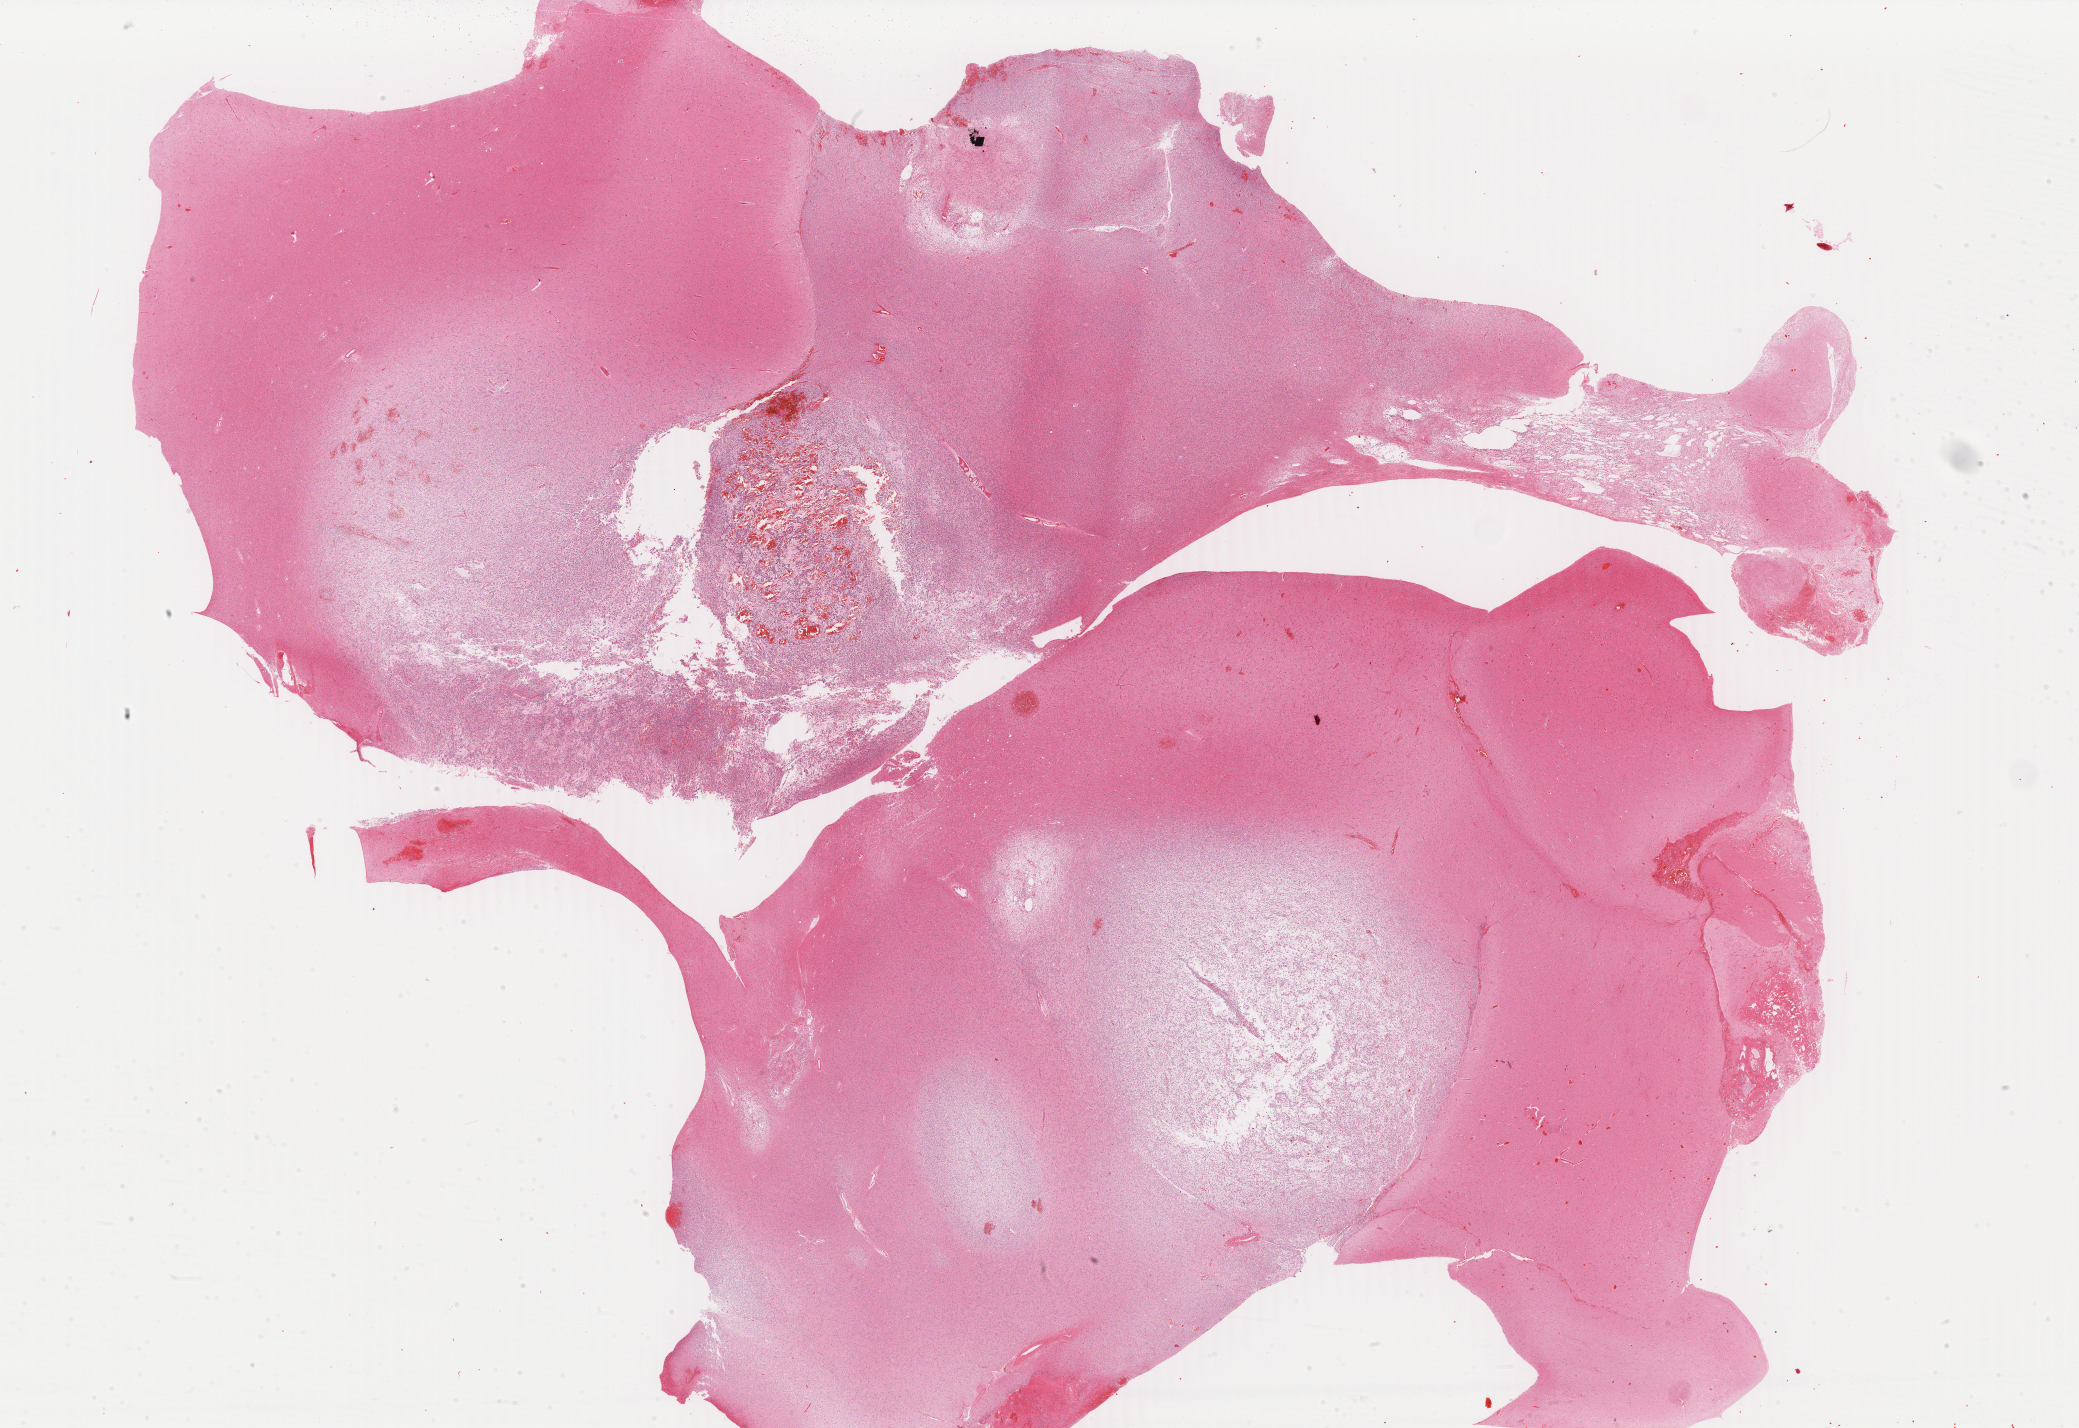
Whole-slide histology image, Hematoxylin and eosin (H&E) stained — low-resolution overview of the scanned area, about 33.1 x 22.7 mm; formalin-fixed paraffin-embedded (FFPE) diagnostic section; sample: primary tumour, brain. Patient: female, age at initial diagnosis 48 years. Histologic grade: G2 (moderately differentiated).
Histologic diagnosis: Oligodendroglioma, NOS.